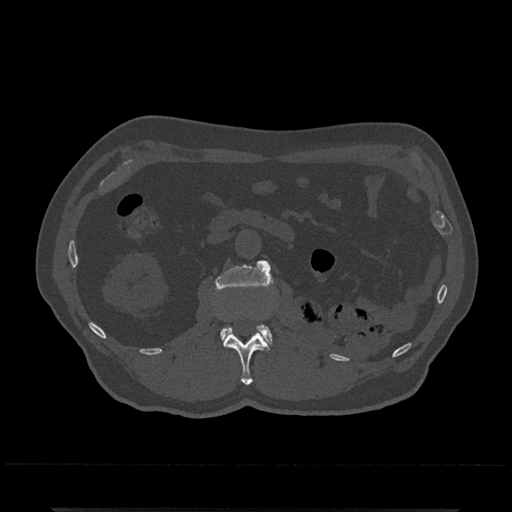
CT including the spine, one axial slice. Position 331 of 797 along the scan axis. Bone window (W 1800 / L 400 HU). 0.5 mm slice thickness. 512 × 512 image matrix. Patient: male, 67 years. From the clinical record (not read from this slice): primary cancer: prostate.
Annotated regions visible in this slice (semi-automatic segmentation, software-assisted and operator-edited):
- L1 vertebra: bounding box (x1, y1, x2, y2) in pixels: (223, 331, 269, 385)
- L2 vertebra: (214, 260, 273, 346)